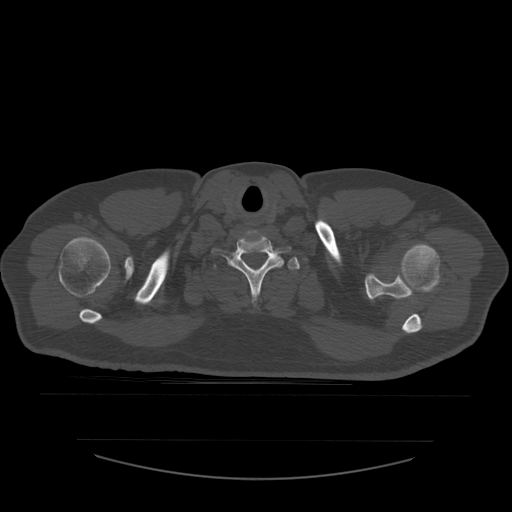
CT including the spine, one axial slice; position 480 of 532 along the scan axis; 120 kVp; bone window (W 1800 / L 400 HU); 1.25 mm slice thickness; 512 × 512 image matrix. Patient age 44 years. Case-level facts recorded for this patient, not image findings: primary cancer: soft tissue sarcoma.
Annotated regions visible in this slice (semi-automatic segmentation, software-assisted and operator-edited):
- T1 vertebra: bounding box (x1, y1, x2, y2) in pixels: (215, 257, 301, 270)